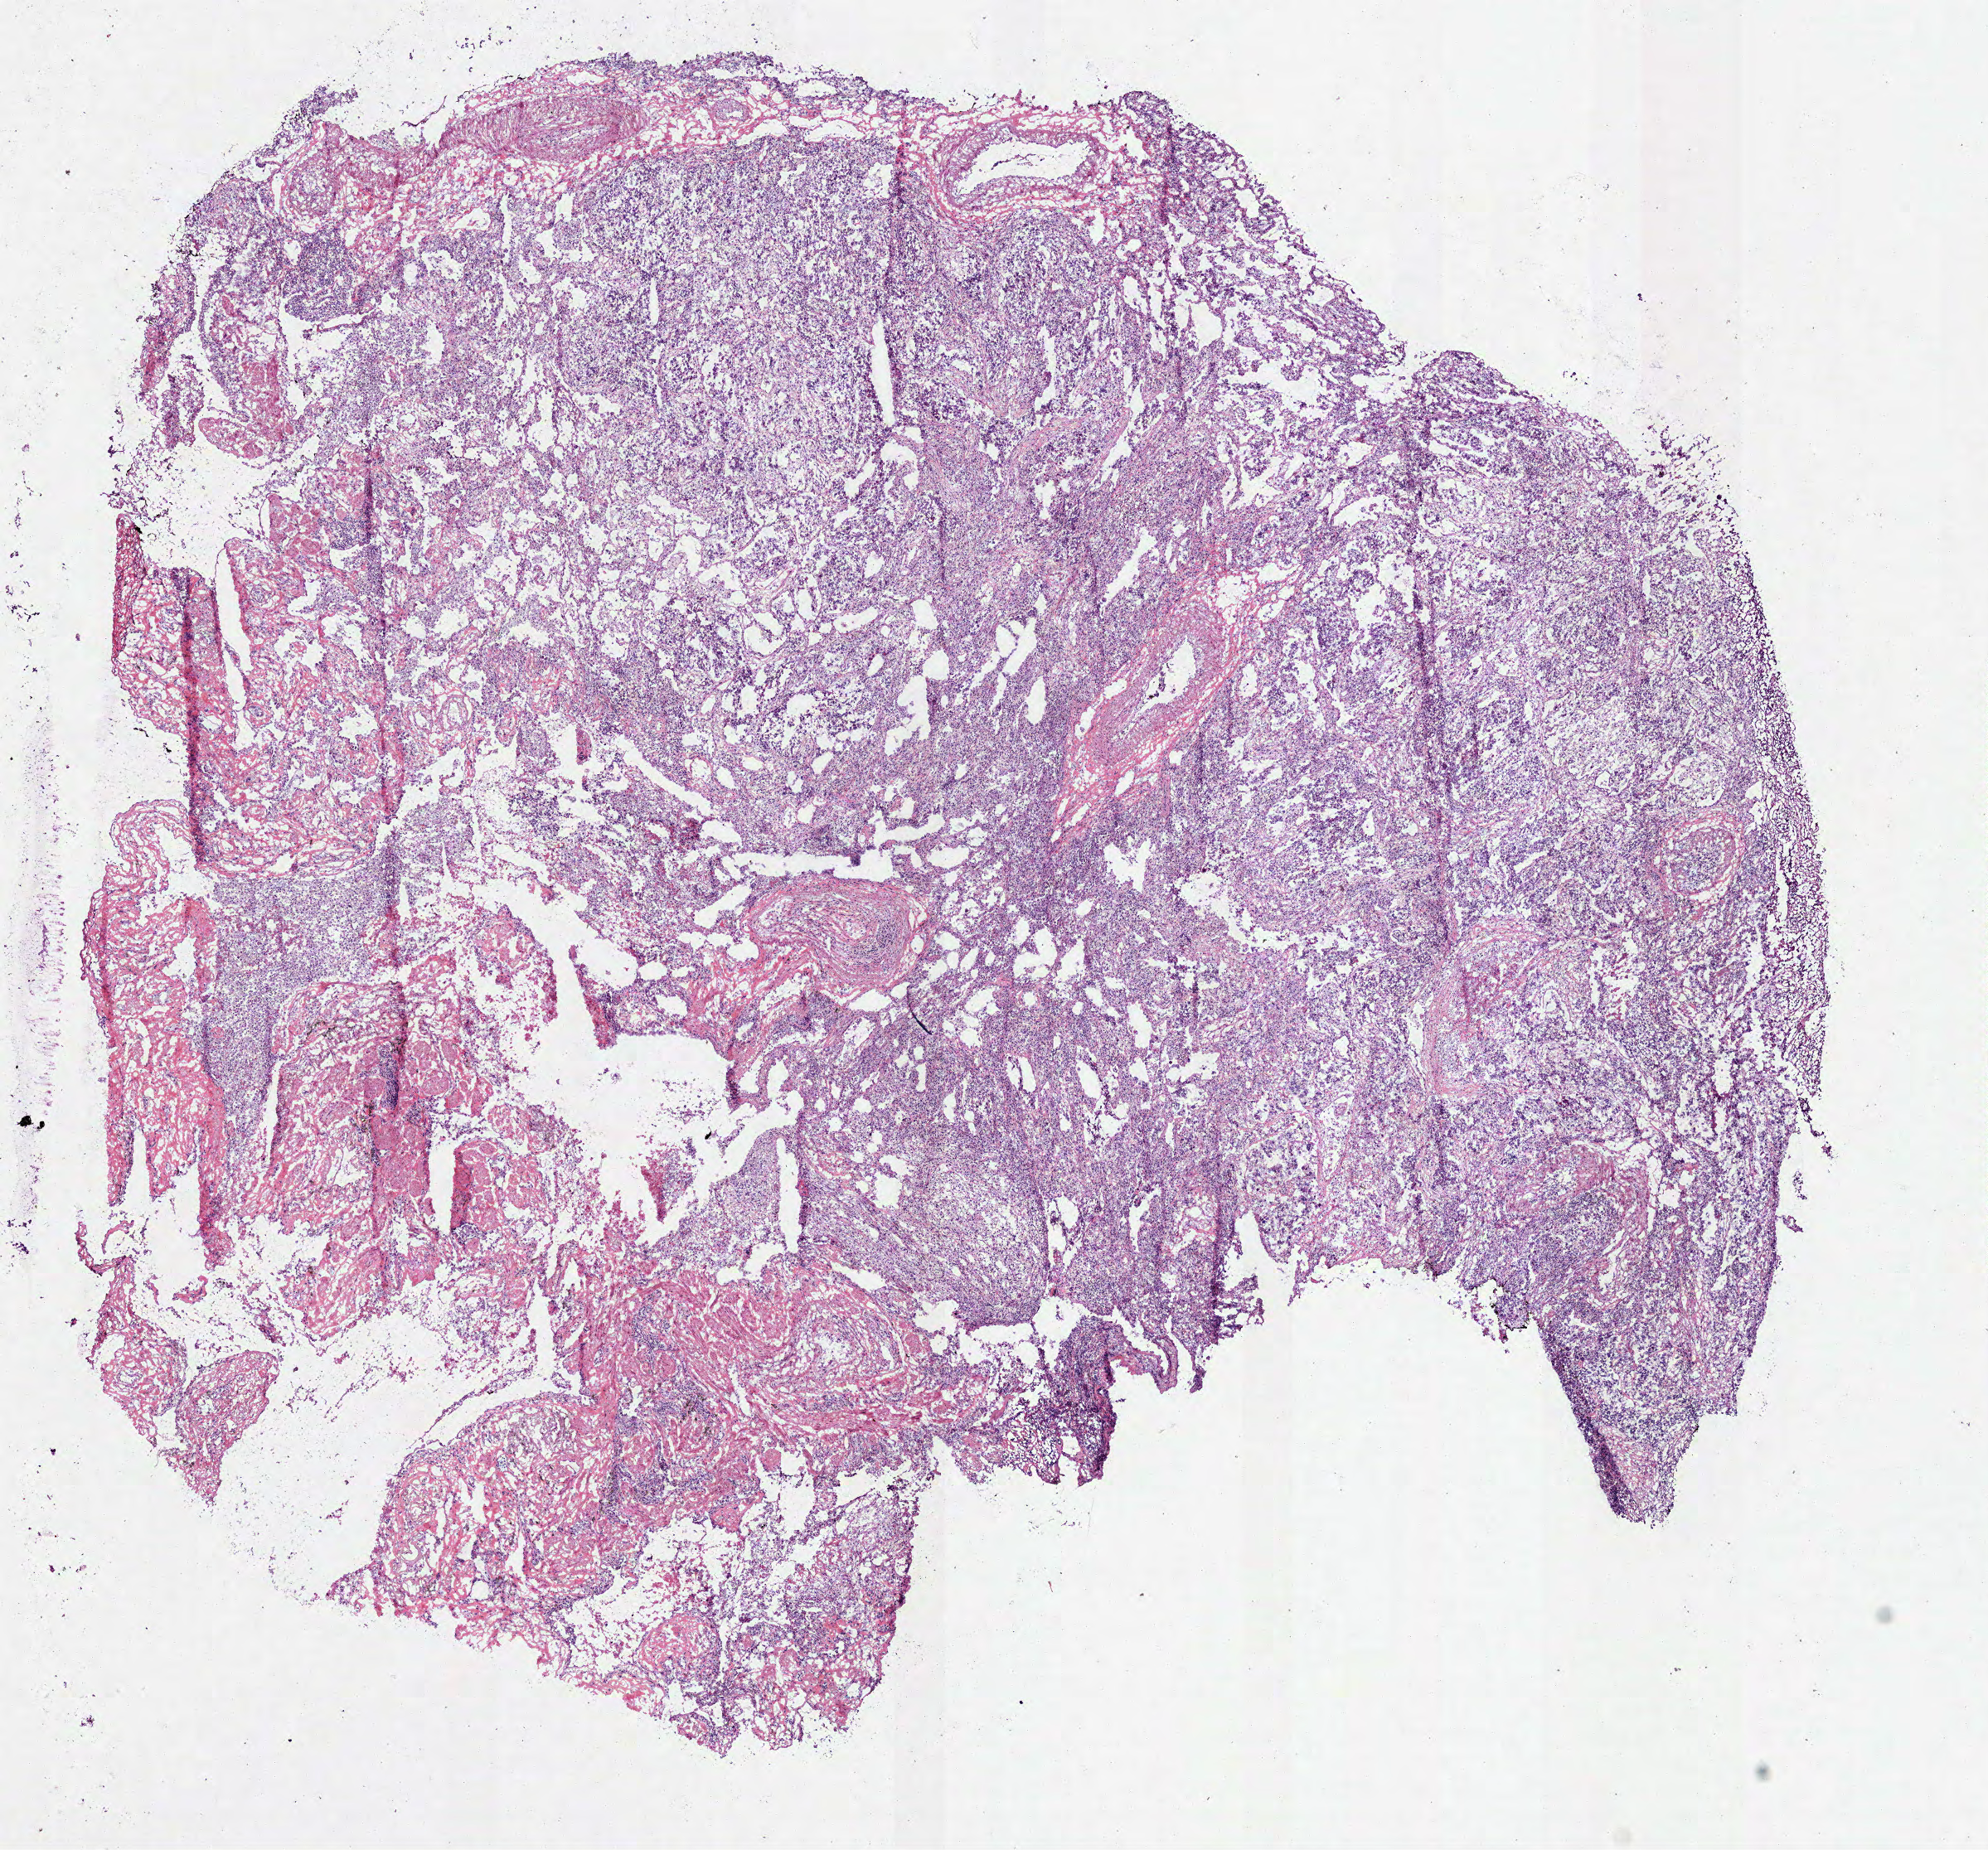
Hematoxylin and eosin (H&E) stained whole-slide image, low-resolution overview of the scanned area, about 9.7 x 9.0 mm (slide scanned at 40x). Frozen section from the bottom of the tissue portion. Primary tumour sample from the lung. Male patient; age at initial diagnosis 67 years. Pathologist review of this section (percent, as recorded): tumour cells 85%, tumour nuclei 70%, normal cells 0%, stromal cells 15%, necrosis 0%.
AJCC pathologic stage: IIA (7th edition). Laterality: right. Histologic diagnosis: Squamous cell carcinoma, NOS (upper lobe, lung).